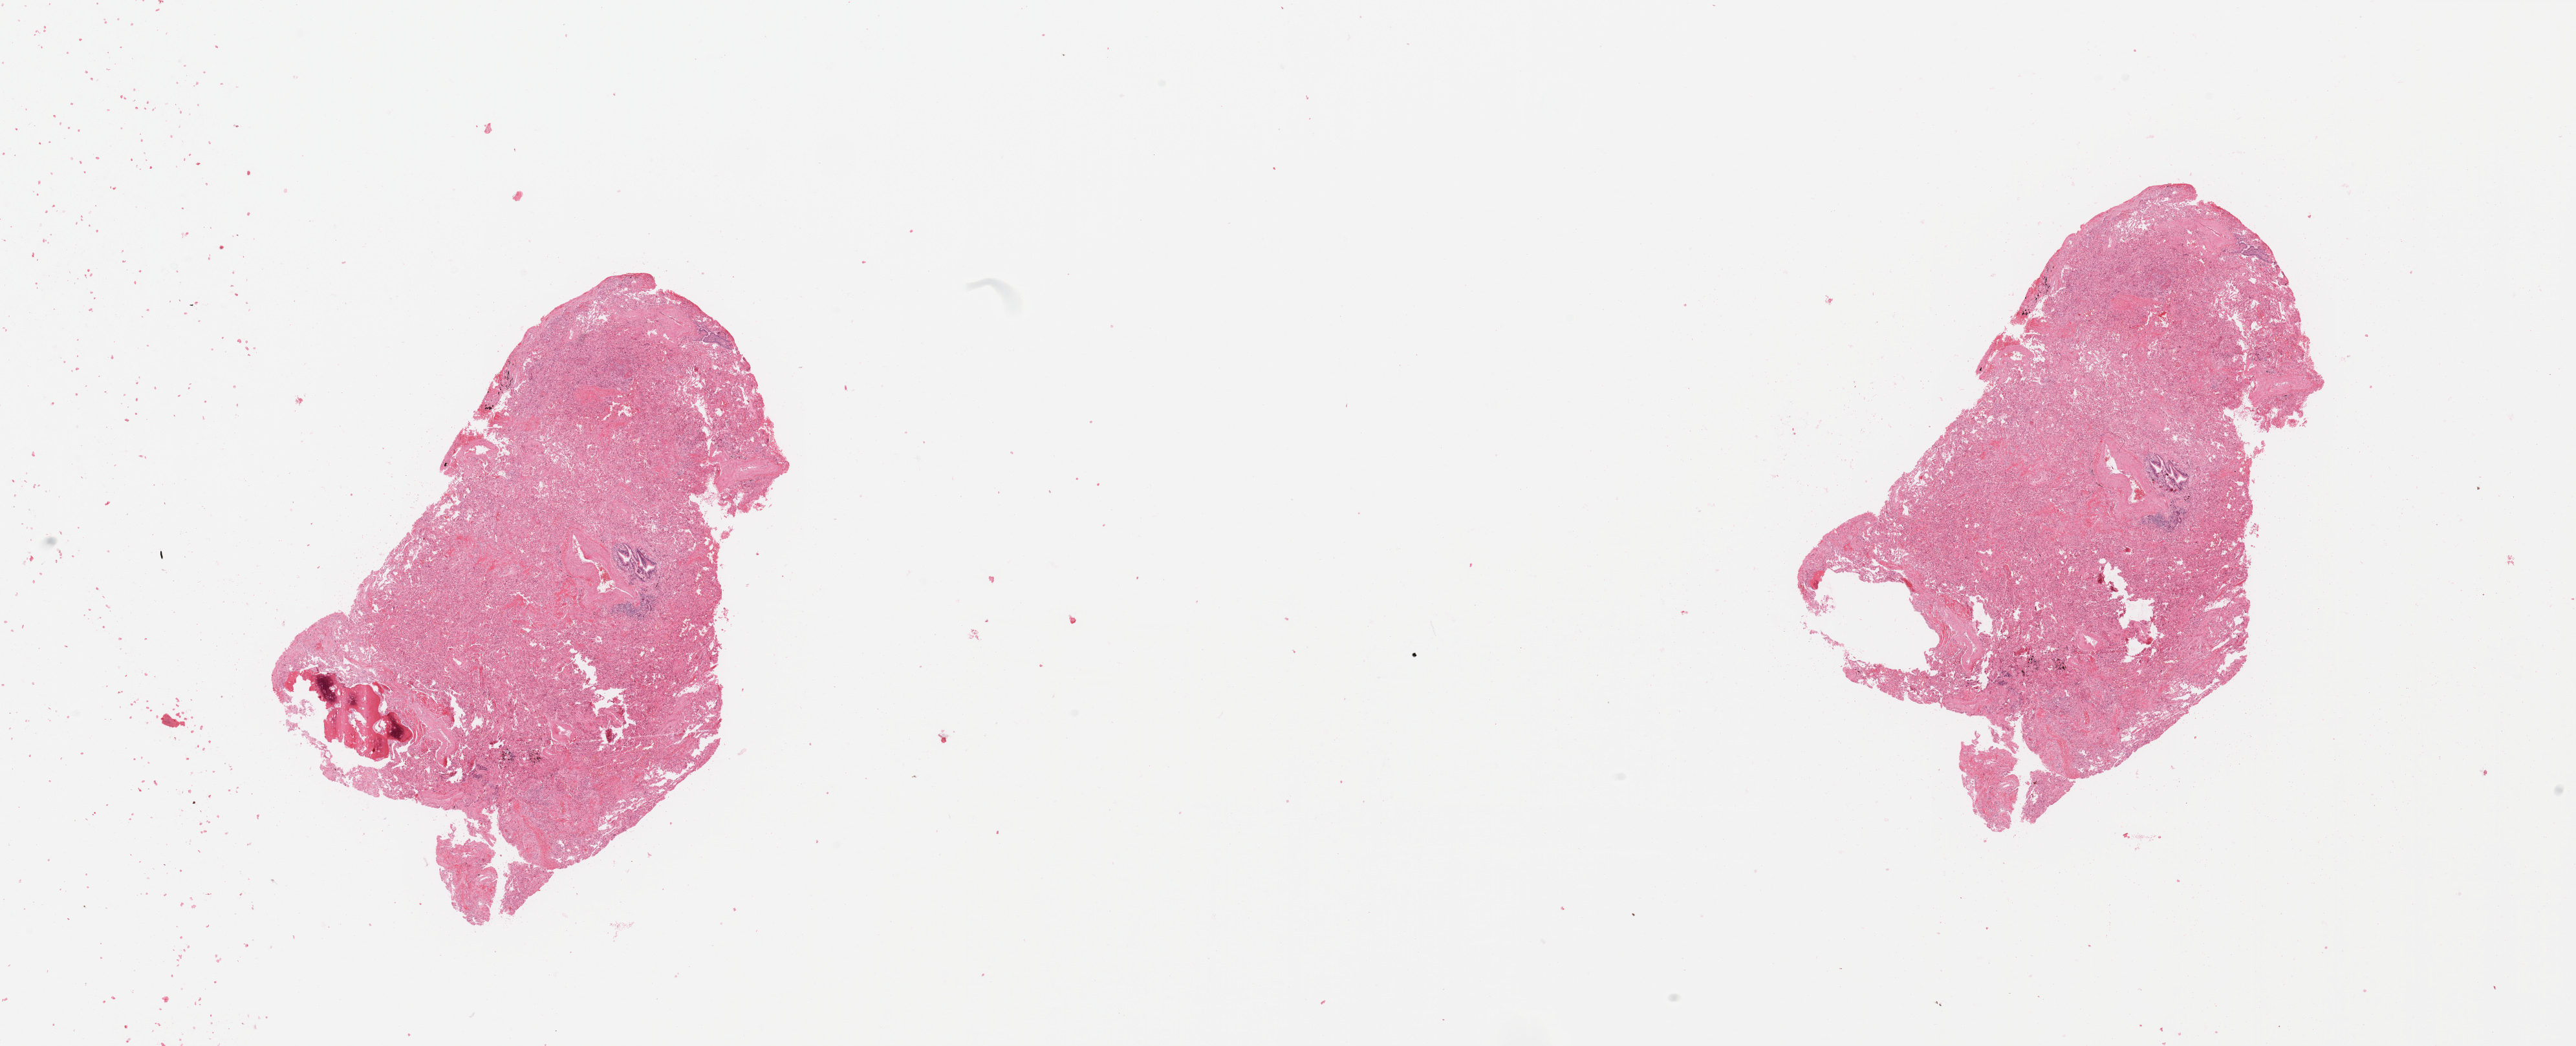
Digitized Hematoxylin and eosin (H&E) stained tissue section (whole slide), a low-resolution overview of the entire scanned area, about 31.5 x 12.8 mm (acquisition: 20x scan); normal (non-tumour) tissue sample, sampled site: lung. Male, 67 y/o.
This section: normal (non-tumour) tissue from the same patient. Patient diagnosis: Adenocarcinoma, NOS.